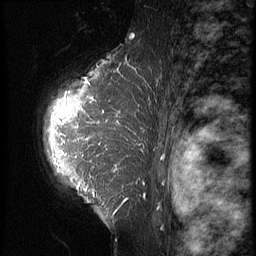
Breast MRI (dynamic contrast-enhanced), one sagittal slice. Slice 47 of 64 in the series (ordered by position). 3 images stored at this slice position (order not interpretable as contrast timing). 1.5 T. TE 4.2 ms, TR 9 ms. 256 × 256 image matrix, field of view 180 × 180 mm. Patient: female, 39 years. Case-level facts recorded for this patient, not image findings: setting: breast cancer imaged before/during neoadjuvant chemotherapy; receptor status: HER2-positive.
Annotated regions visible in this slice (semi-automatic segmentation, software-assisted and operator-edited):
- analysis volume of interest (the breast-tissue region the enhancement analysis was run in; not a lesion): bounding box [x1, y1, x2, y2] px = [36, 47, 149, 239]
- tumour enhancement mask (voxels above the 140 % enhancement threshold inside the analysis volume of interest): [61, 97, 142, 213]